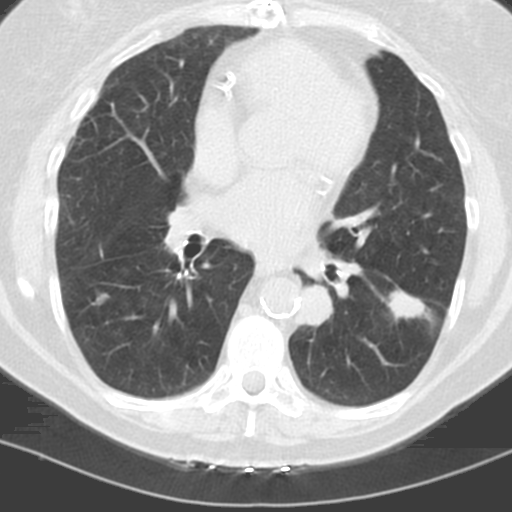
Low-dose screening chest CT, one axial slice; position 54 of 121 along the scan axis; lung window (W 1500 / L -600 HU); 3.2 mm slice thickness; 512 × 512 image matrix, field of view 278 × 278 mm.
Outlined on this slice (expert manual segmentation):
- lesion 1 (tumor, lower lobe of left lung): bounding box <388,291,424,319> (left, top, right, bottom; pixels)
- lesion 2 (tumor, lower lobe of left lung): <303,286,333,326>